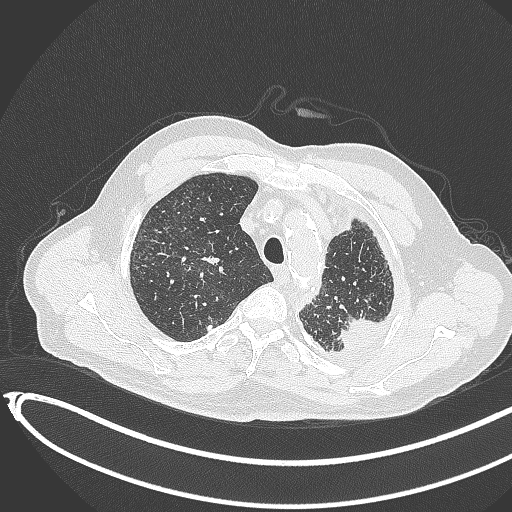
Chest CT, one axial slice; position 349 of 451 along the scan axis; reconstruction kernel B70f; lung window (W 1500 / L -600 HU); 1 mm slice thickness; 512 × 512 image matrix, field of view 400 × 400 mm. Male patient, age 78 years. From the clinical record (not read from this slice): clinical TNM (as recorded): T1c N0 M1.
Annotated regions visible in this slice (bounding box drawn by a radiologist):
- lung tumour (recorded histology: adenocarcinoma): box from (x=339, y=314) to (x=382, y=357) px